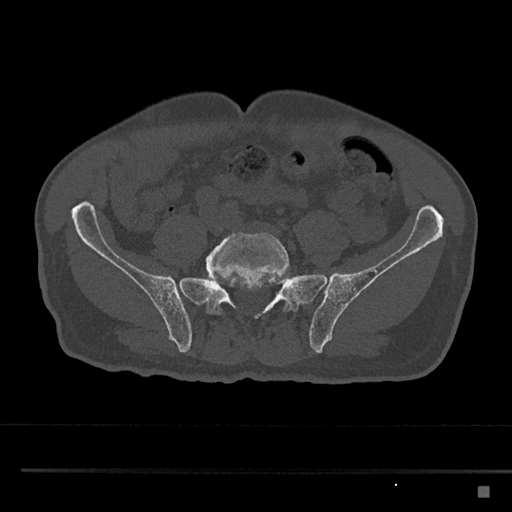
CT including the spine, one axial slice; position 556 of 797 along the scan axis; reconstruction kernel Br40s/3; 120 kVp; bone window (W 1800 / L 400 HU); 0.5 mm slice thickness; 512 × 512 image matrix, field of view 391 × 391 mm. Male patient, age 59 years. Case-level facts recorded for this patient, not image findings: primary cancer: prostate.
Structures marked on this image (semi-automatic segmentation, software-assisted and operator-edited):
- L5 vertebra: bounding box [x1, y1, x2, y2] px = [206, 232, 291, 315]